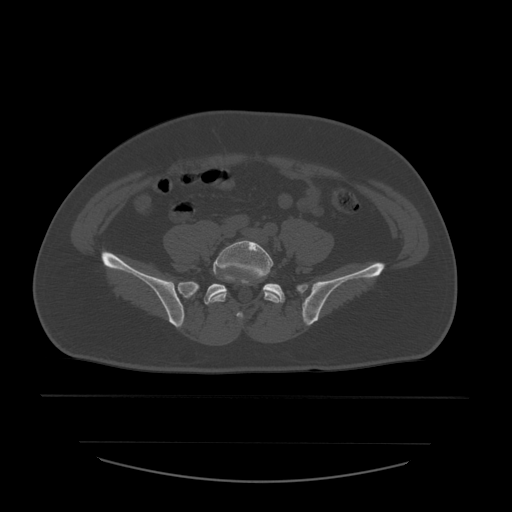
CT including the spine, one axial slice. Position 111 of 532 along the scan axis. Reconstruction kernel STANDARD. Bone window (W 1800 / L 400 HU). 1.25 mm slice thickness. 512 × 512 image matrix, field of view 441 × 441 mm. Patient age 44 years. Case-level facts recorded for this patient, not image findings: primary cancer: soft tissue sarcoma.
Annotated regions visible in this slice (semi-automatic segmentation, software-assisted and operator-edited):
- L5 vertebra: bounding box <211,241,280,303> (left, top, right, bottom; pixels)